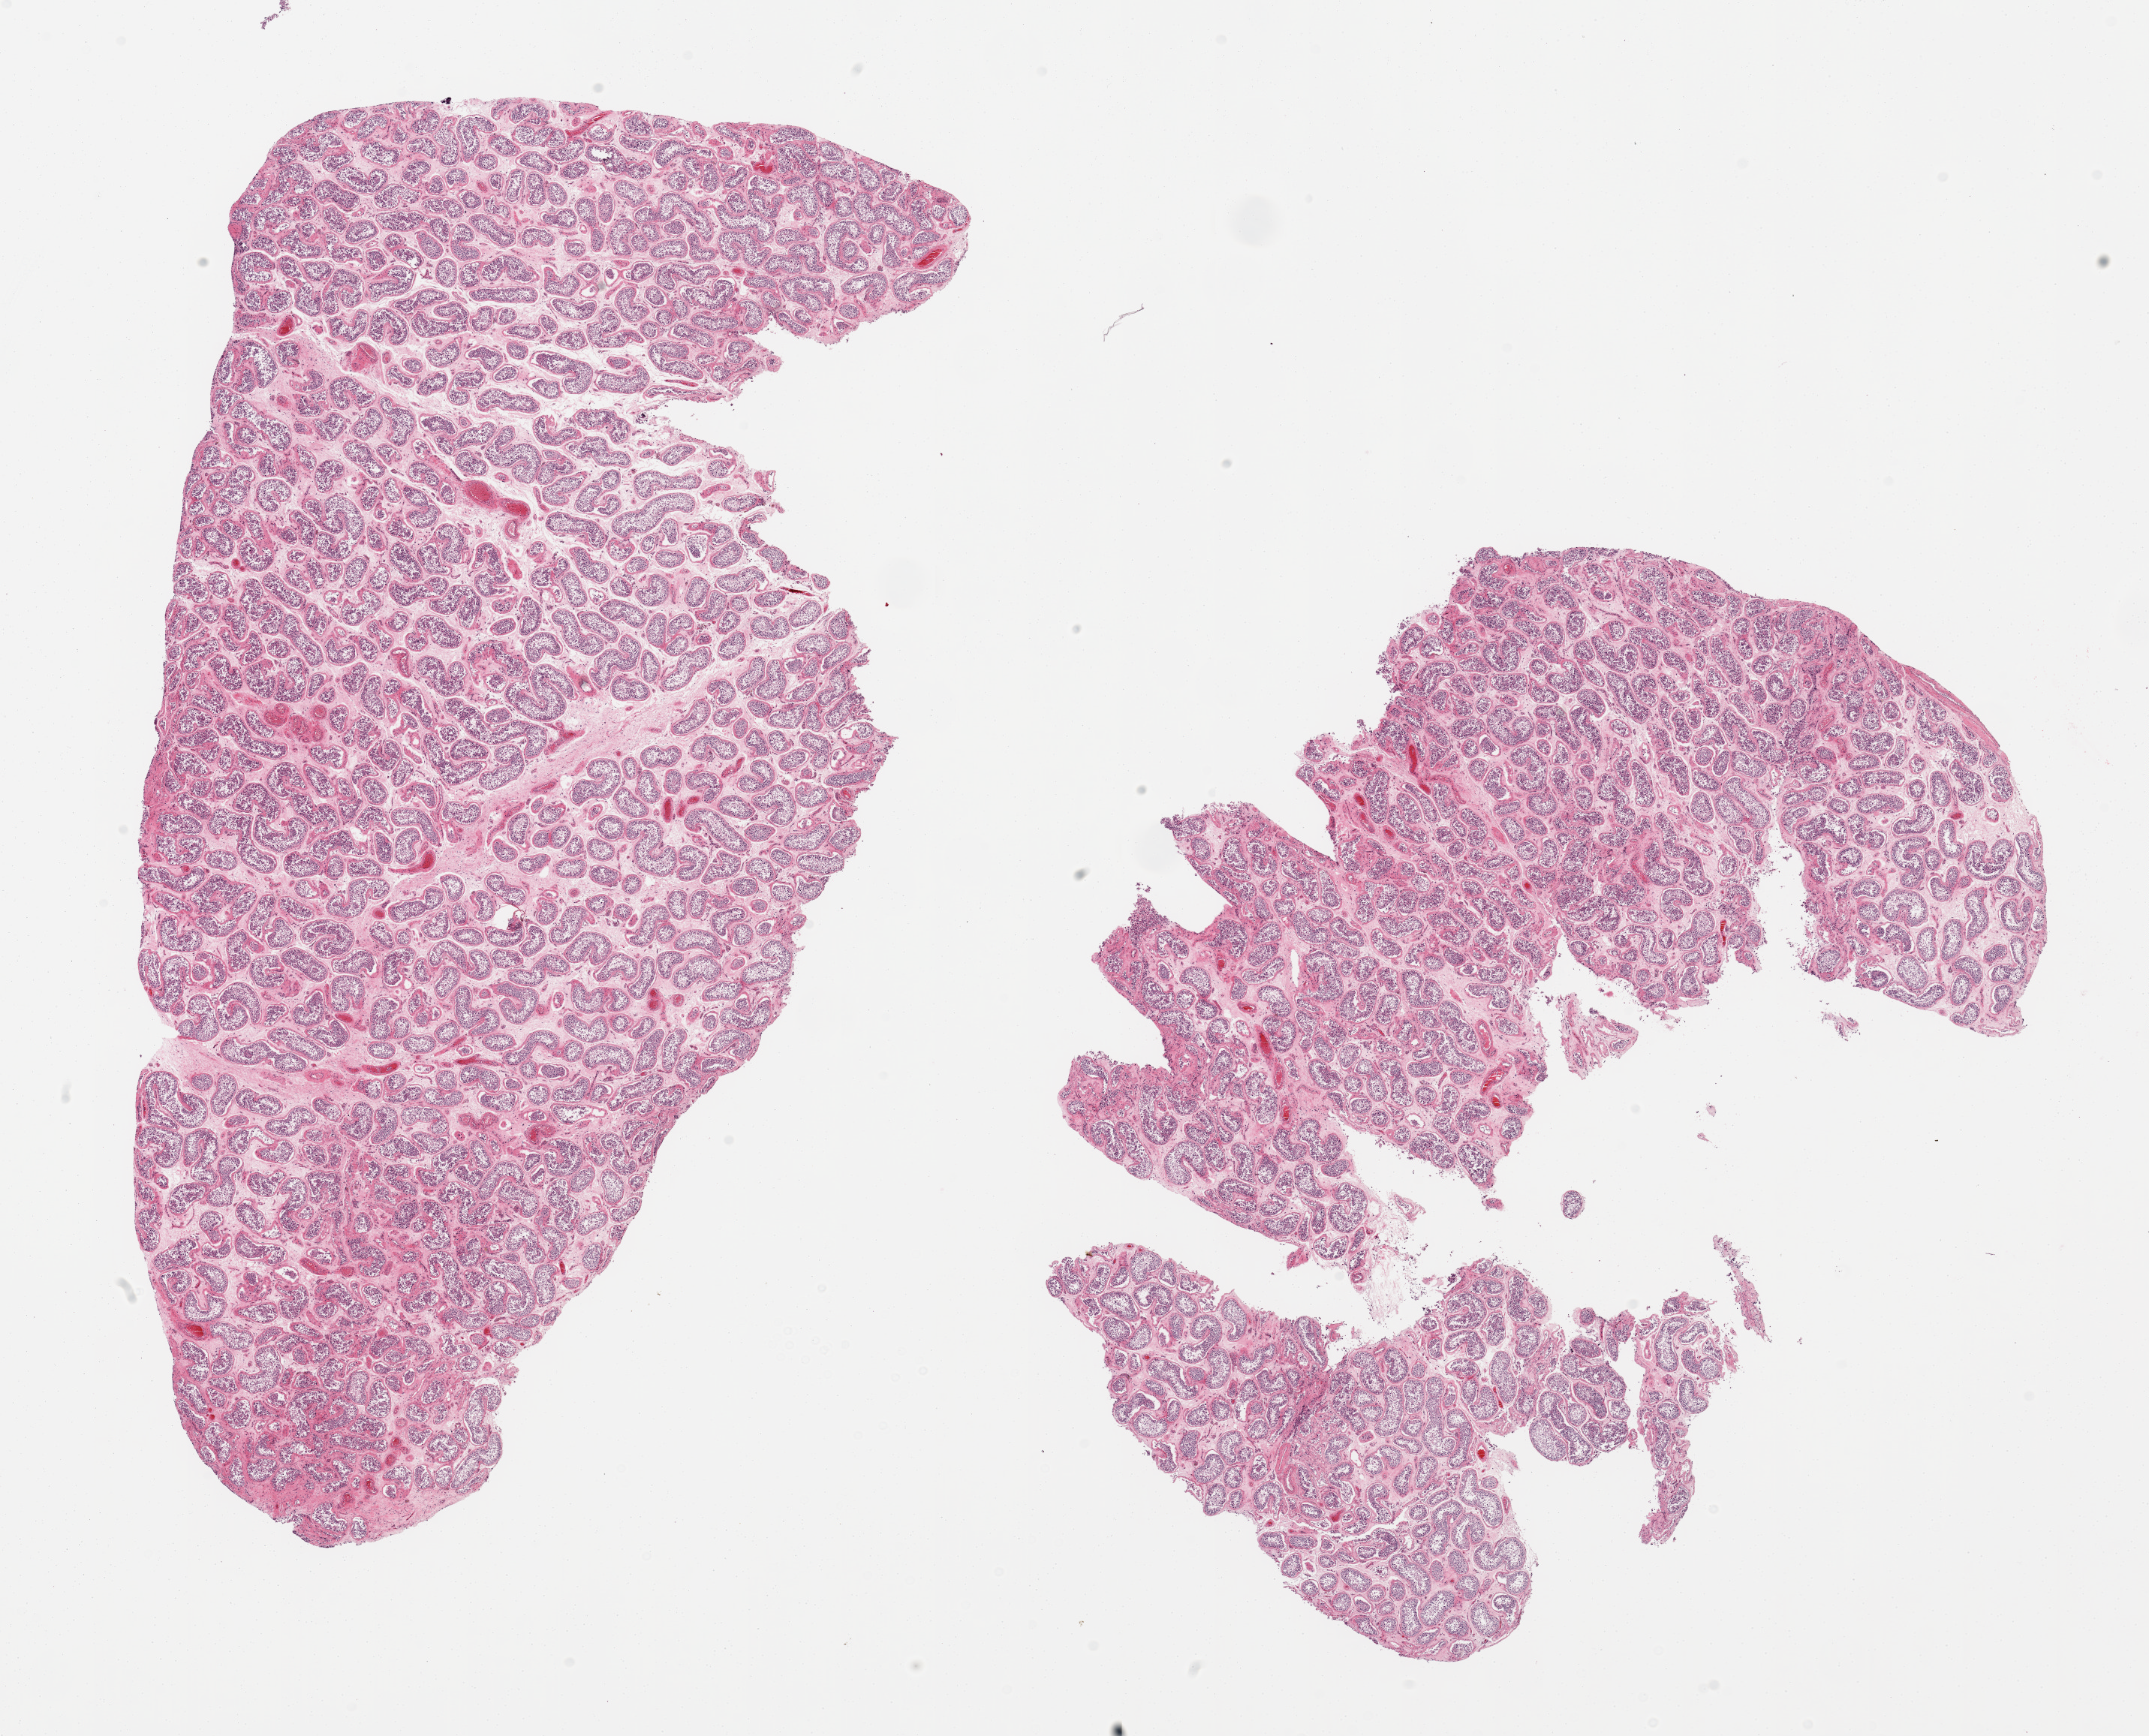
Hematoxylin and eosin (H&E) whole-slide image — a low-resolution overview of the entire scanned area, about 22.6 x 18.3 mm. PAXgene-fixed paraffin-embedded (PFPE) section. Sampled site (target tissue): testis. Tissue donor sample. Male donor.
Reviewer comment on this tissue sample: 2 pieces; spermatogenesis present.